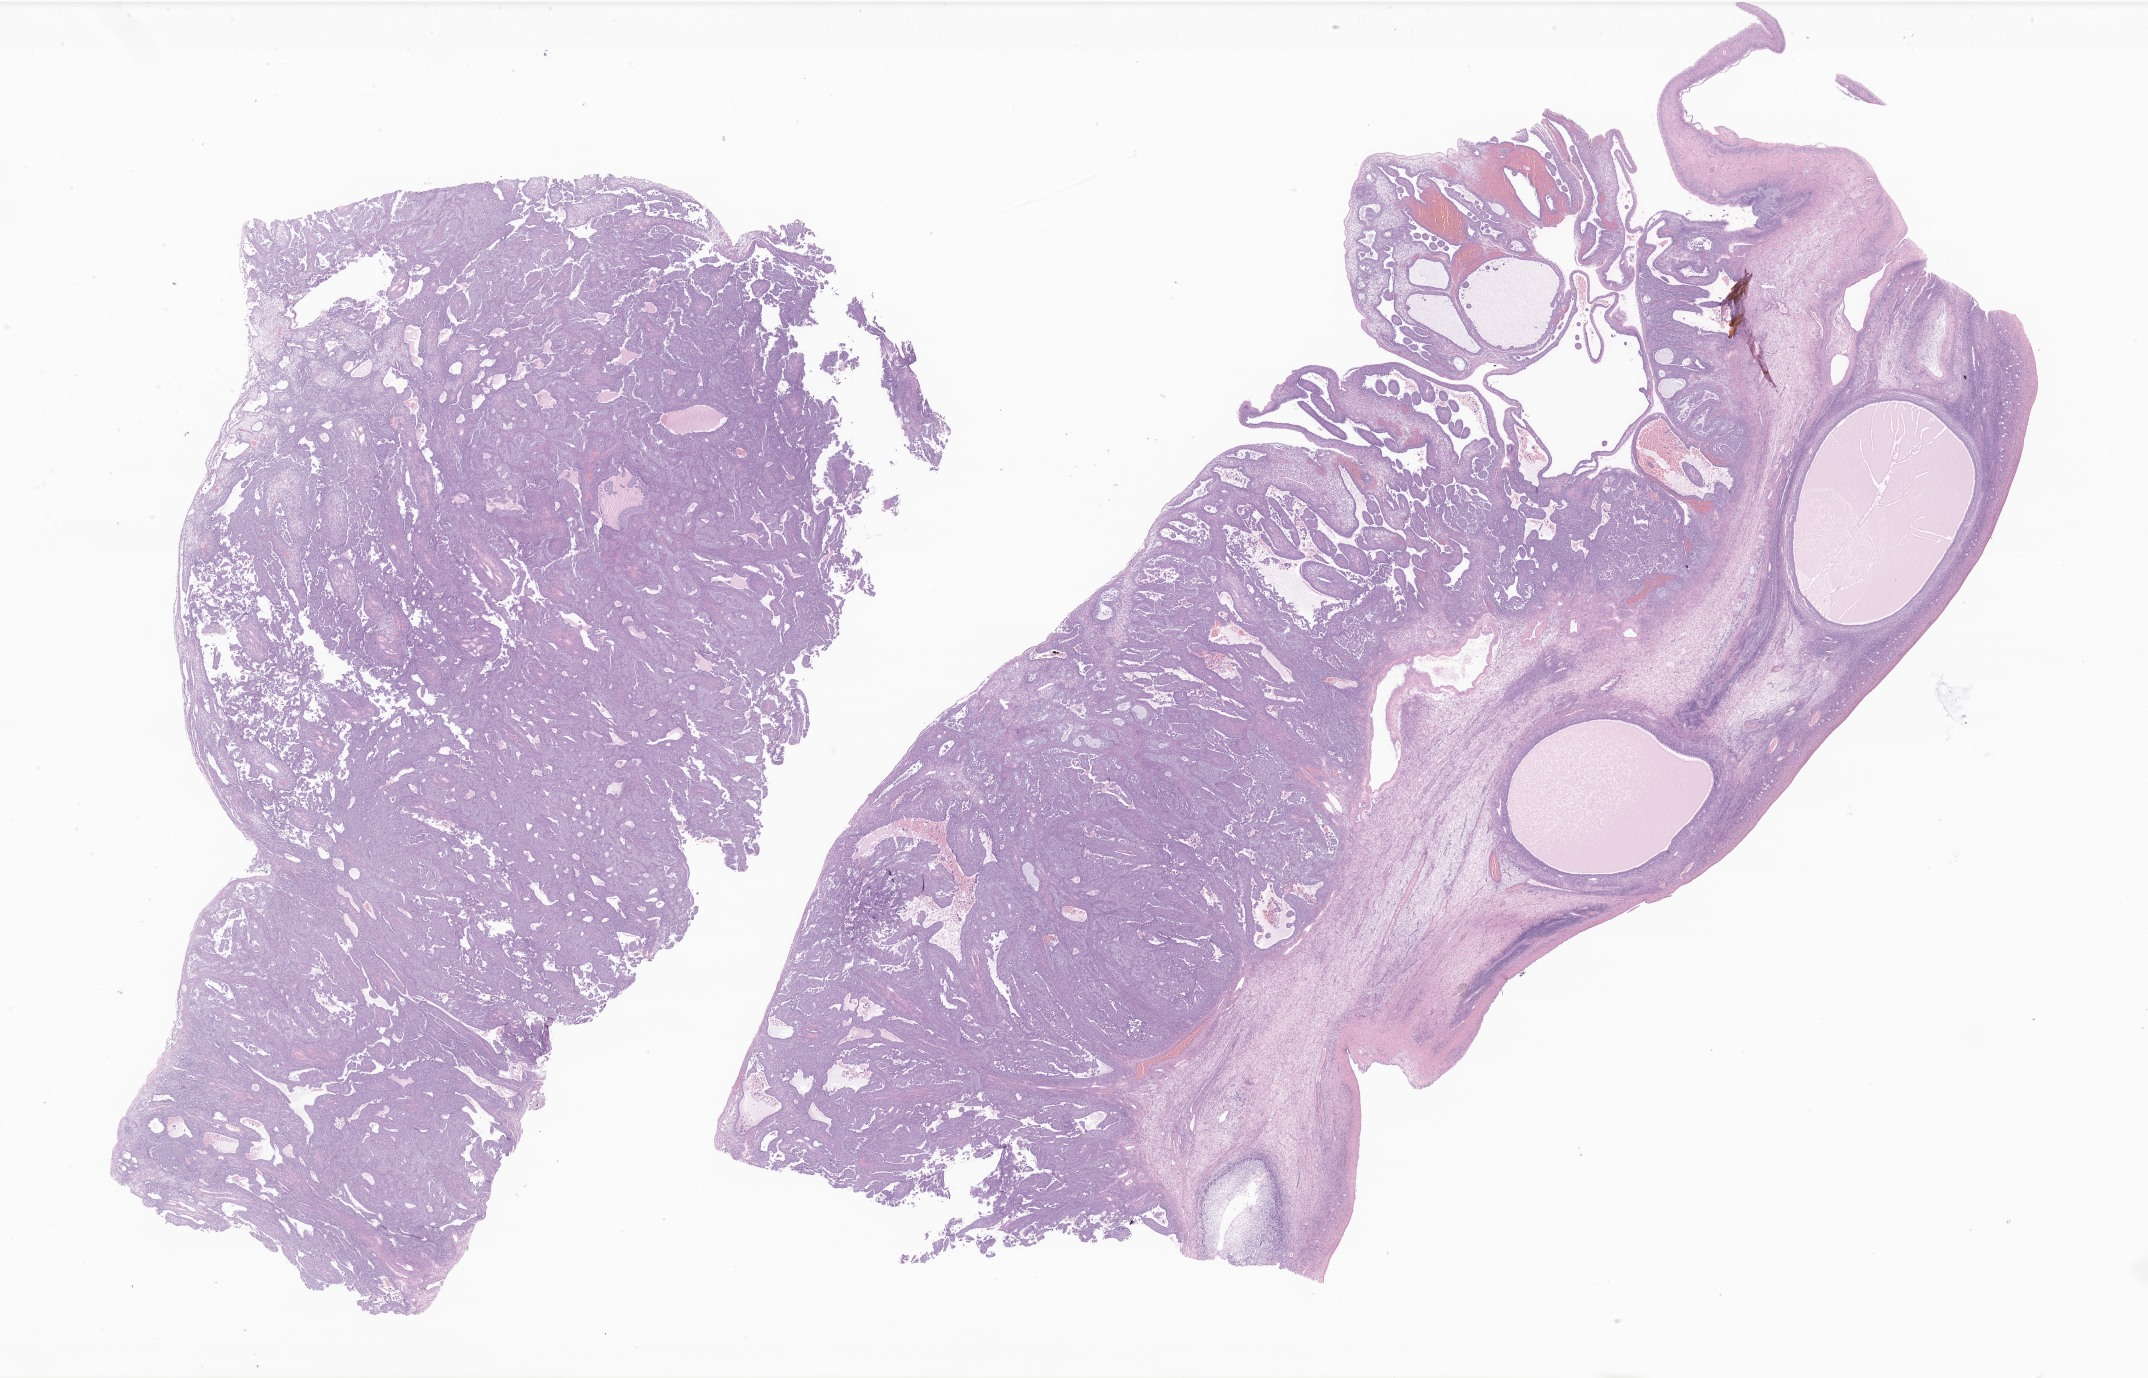
Whole-slide image, haematoxylin and eosin stain of tumor tissue from the ovary — a low-resolution overview of the entire scanned area, about 36.2 x 23.2 mm. Formalin-fixed paraffin-embedded section. Patient female; age 168 months.
* diagnosis: Granulosa cell tumor, juvenile